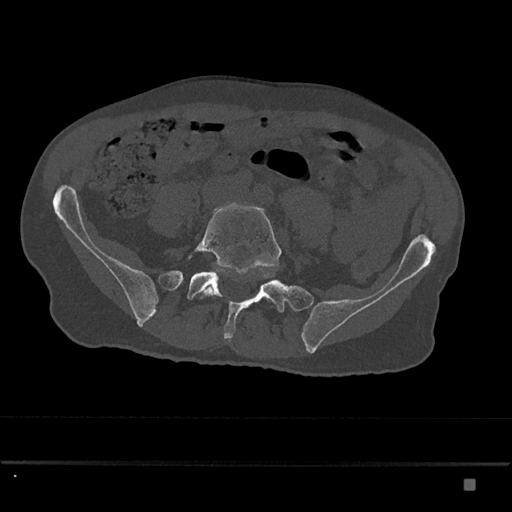
CT including the spine, one axial slice; slice 257 of 797 in the series (ordered by position); bone window (W 1800 / L 400 HU); 512 × 512 image matrix, field of view 390 × 390 mm. Male patient, age 72 years. Case-level facts recorded for this patient, not image findings: primary cancer: prostate.
Outlined on this slice (semi-automatic segmentation, software-assisted and operator-edited):
- L5 vertebra: bounding box <188,204,282,299> (left, top, right, bottom; pixels)